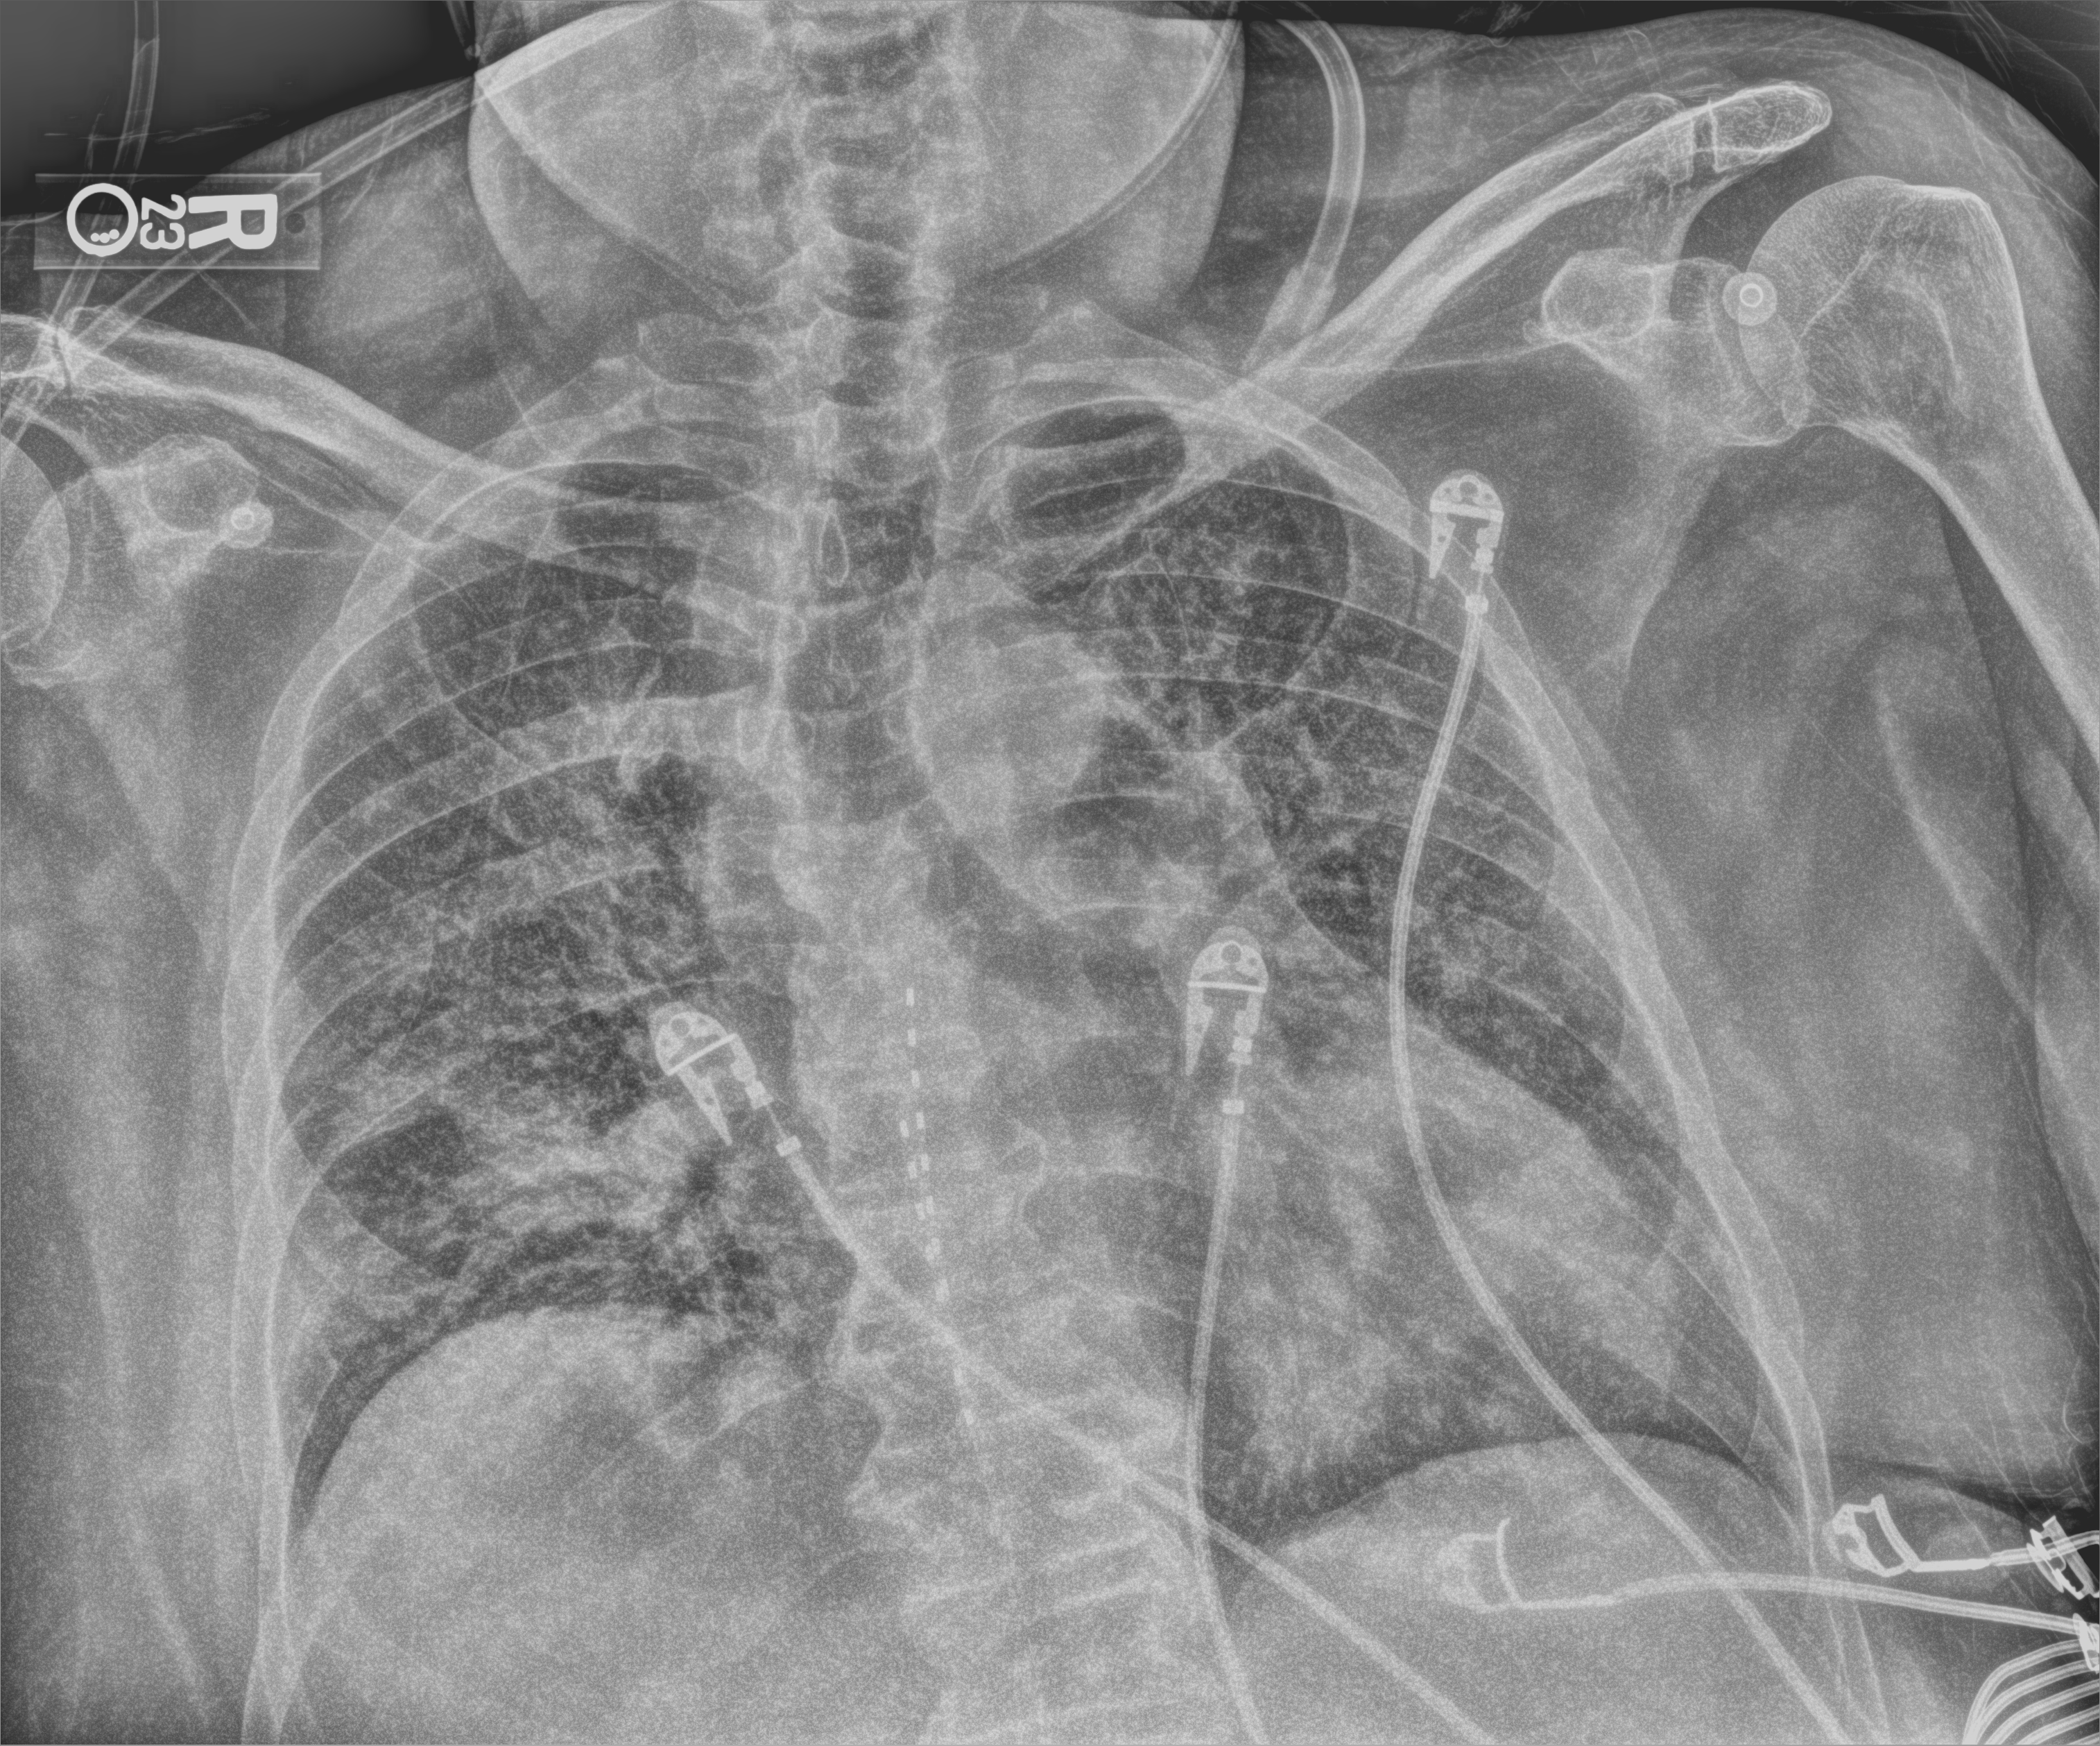
Portable chest radiograph; anteroposterior (AP) projection. Patient hospitalised with COVID-19; male, aged 60–74 years.
From the hospital-stay record, not from the radiograph (when in the stay this image was taken is not recorded):
- length of hospital stay: 3 days
- admitted to intensive care during this hospital stay: no
- mechanically ventilated during this hospital stay: no